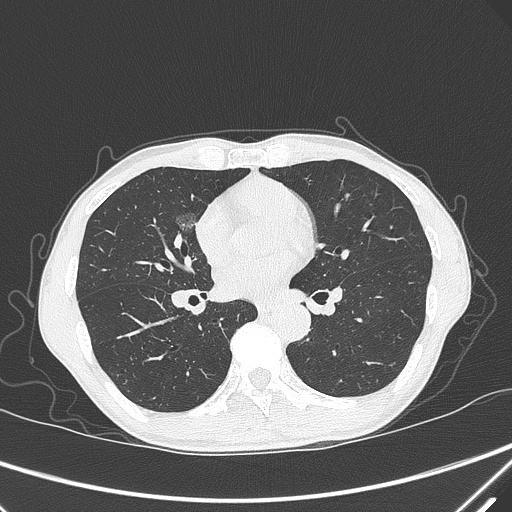
Chest CT, one axial slice. Slice 163 of 339 in the series (ordered by position). 120 kVp. Lung window (W 1500 / L -600 HU). 1 mm slice thickness. 512 × 512 image matrix. Patient: male, 67 years. From the clinical record (not read from this slice): clinical TNM (as recorded): T1c N0 M0; histopathological grade: G1-2.
Outlined on this slice (bounding box drawn by a radiologist):
- lung tumour (recorded histology: adenocarcinoma): box from (x=164, y=205) to (x=201, y=239) px